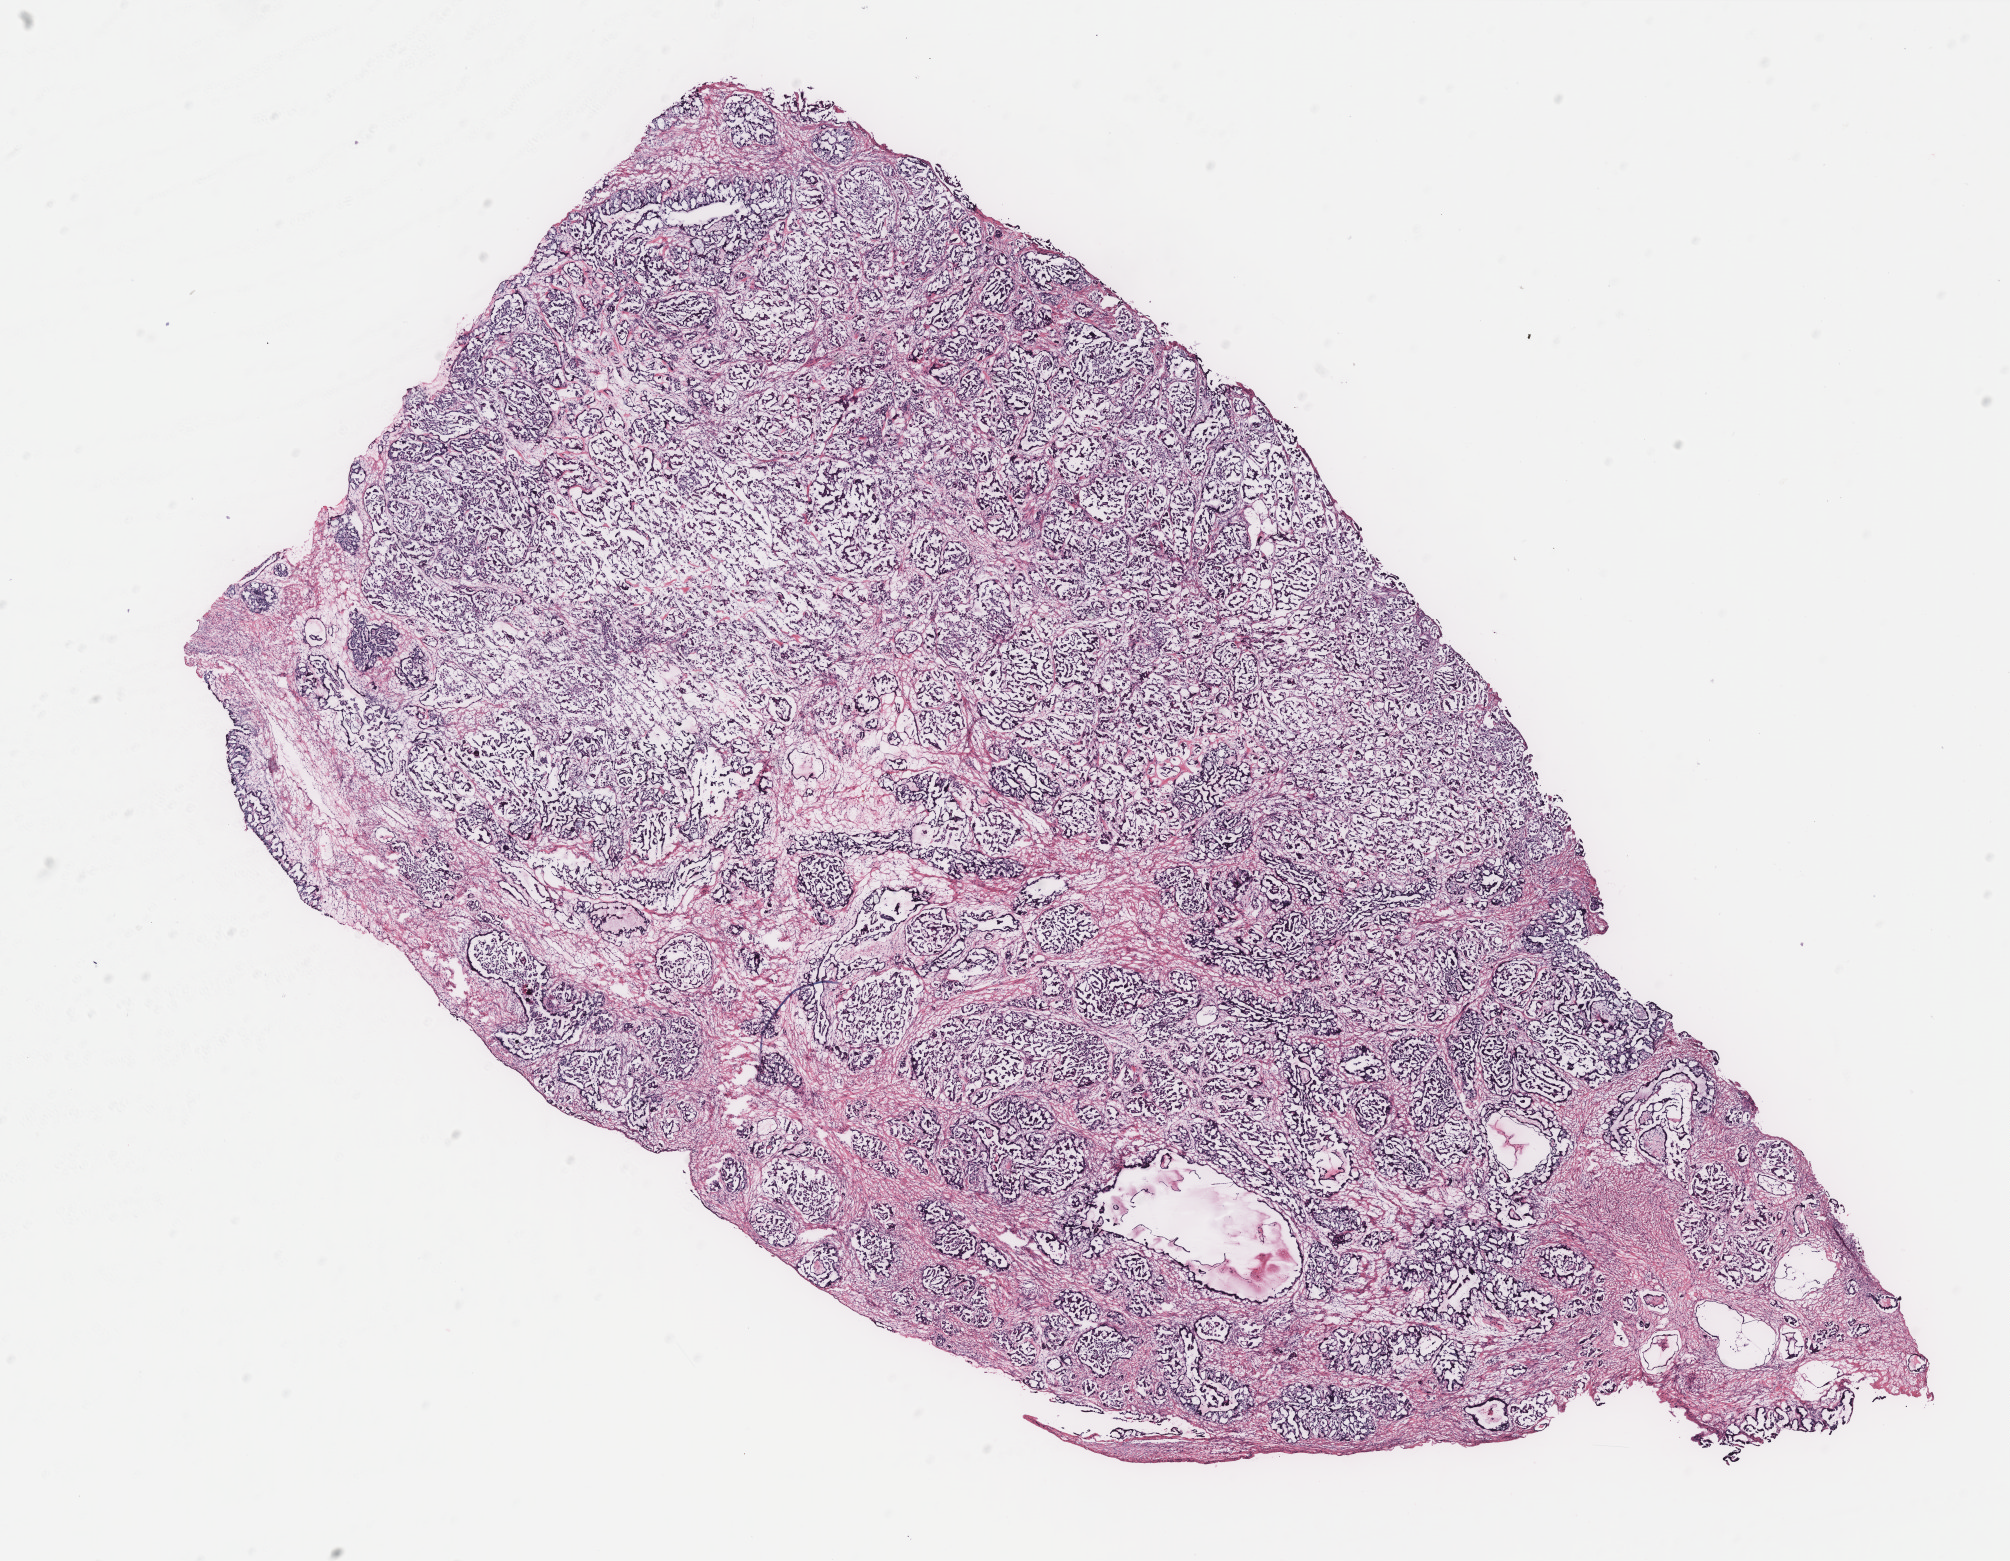
Whole-slide histology image, Hematoxylin and eosin (H&E) stained — shown as a low-resolution overview of the whole scanned area (about 16.1 x 12.5 mm, slide scanned at 40x); ovary, tumour tissue. 73-year-old female patient.
* diagnosis: Serous adenocarcinoma, NOS
* primary tumour site (as recorded): ovary